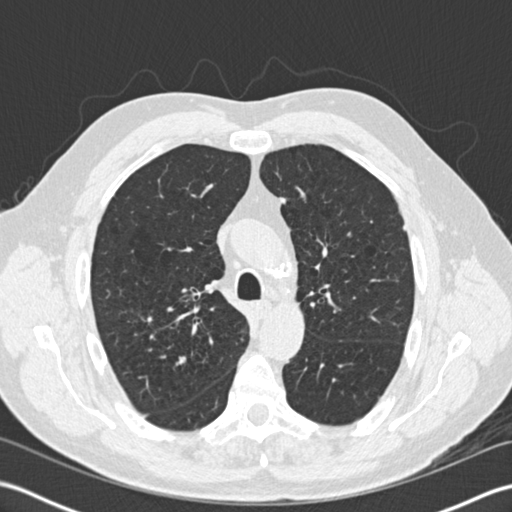
Axial slice from a low-dose chest CT screening exam; second annual screen; lung window (W 1500 / L -600 HU); 2 mm slice thickness; 120 kVp; slice 54 of 204 in the series. Male participant, aged 65 years at enrolment. Former smoker at enrolment.
Expert reader's lesion annotation, bounding box [x1, y1, x2, y2] px = [157, 350, 202, 386]. The screening reader recorded 6 non-calcified nodules or masses ≥4 mm on this exam (right upper lobe, left upper lobe, left upper lobe, right upper lobe, left upper lobe, right upper lobe); which of them this box marks is not recorded. Official screen result: positive, other. Lung cancer was diagnosed 421 days after this screen (after the third annual screen): adenocarcinoma, NOS, right upper lobe, moderately differentiated (G2), stage IA (AJCC 6th edition), 16 mm at pathology.